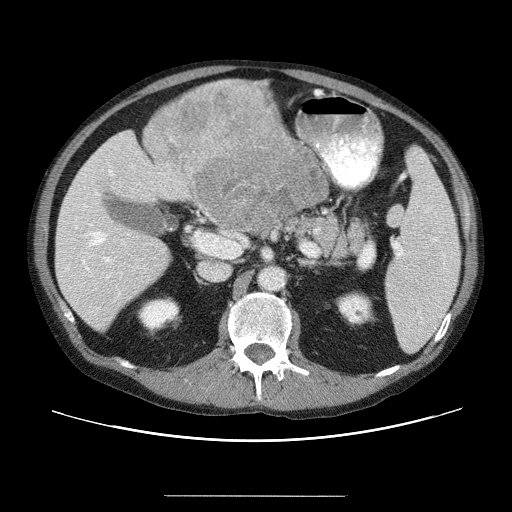
Contrast-enhanced abdominal CT (liver protocol), one axial slice; slice 18 of 69 in the series (ordered by position); 120 kVp; soft-tissue window (W 400 / L 40 HU); 2.5 mm slice thickness; 512 × 512 image matrix, field of view 380 × 380 mm. From the clinical record (not read from this slice): diagnosis: hepatocellular carcinoma (patient treated with transarterial chemoembolisation; whether this scan precedes or follows treatment is not stated here); TNM stage (as recorded): Stage-IVB; Child-Pugh class: B.
Outlined on this slice (semi-automatically segmented with operator editing):
- liver parenchyma outside the tumour (the mass and vessels are separate outlines, so this box may not span the whole liver): box from (x=54, y=134) to (x=324, y=325) px
- mass: (x=143, y=82)–(x=329, y=238)
- liver vessels: (x=69, y=157)–(x=276, y=284)